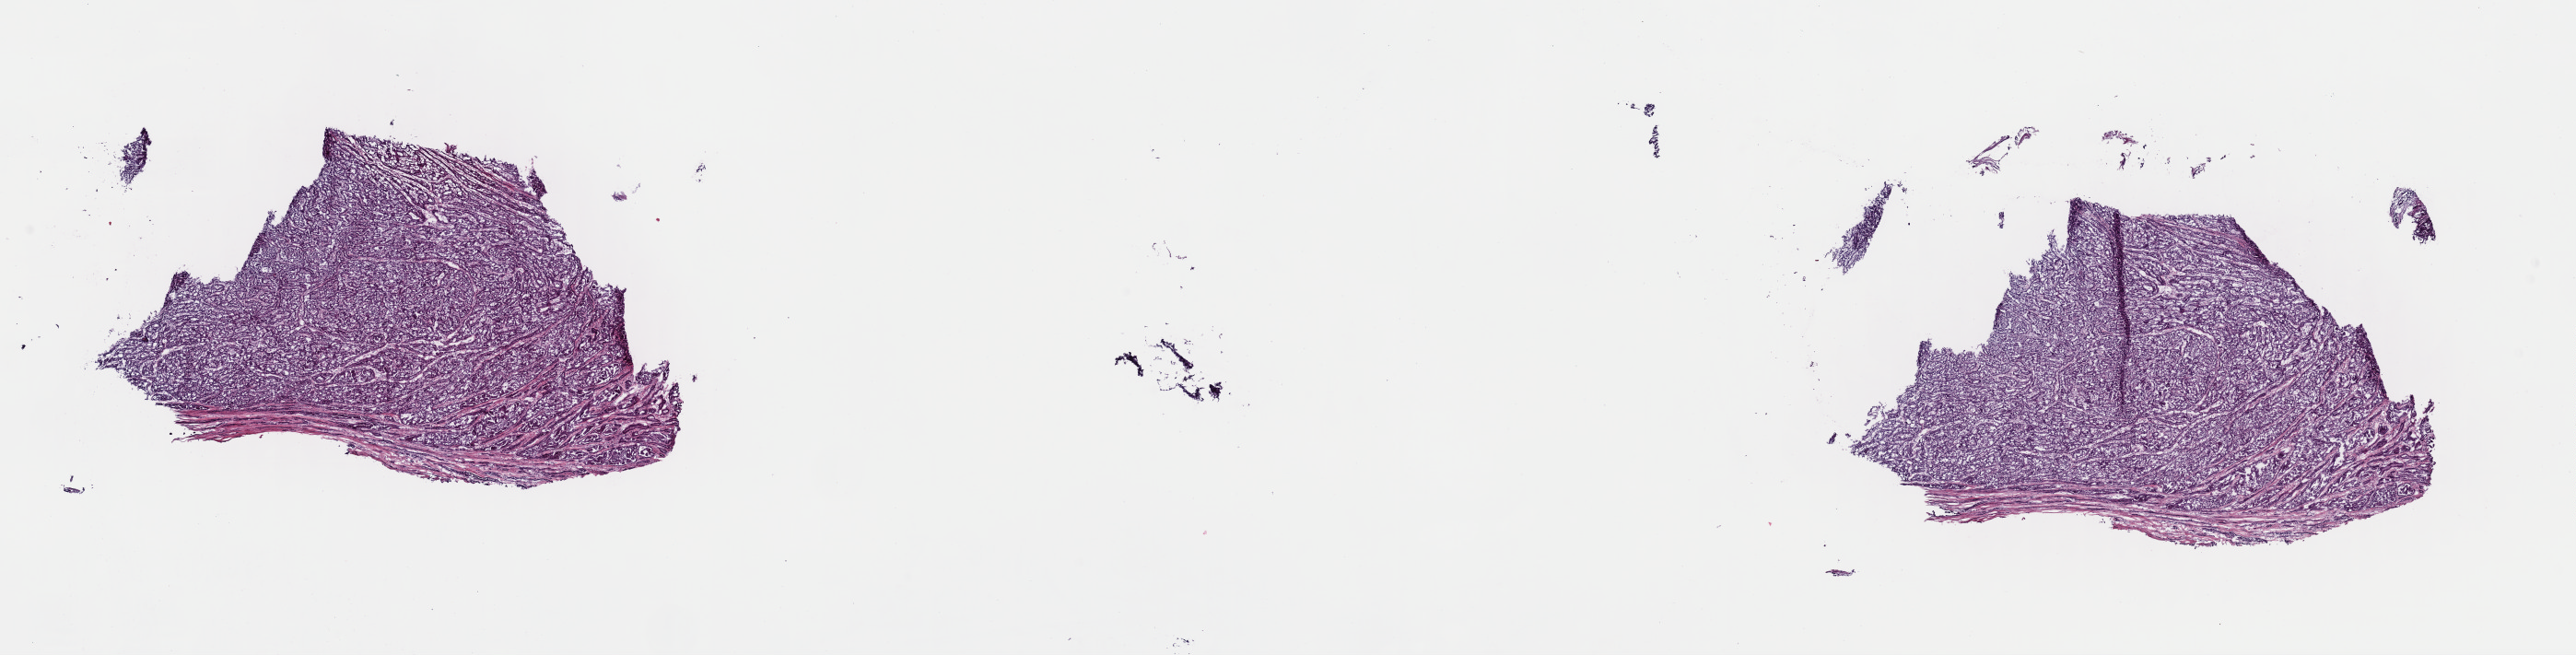
Digitized H&E tissue section (whole slide) — whole scanned area (about 22.1 x 5.6 mm) shown as a low-resolution overview. Frozen section. Sample: primary tumour, kidney. Patient: male, age at initial diagnosis 79 years. Composition of this section per pathologist review: tumour cells 90%, tumour nuclei 100%, normal cells 0%, stromal cells 10%, necrosis 0%. Inflammatory infiltration, as recorded: lymphocyte infiltration 2%, monocyte infiltration 5%, neutrophil infiltration 2%.
* laterality: left
* AJCC pathologic stage: III (7th edition)
* histologic diagnosis: Papillary adenocarcinoma, NOS
* TNM: T3a NX MX